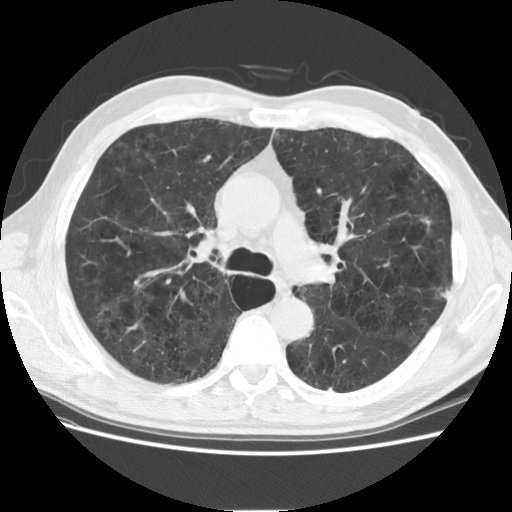
Axial slice from a low-dose chest CT screening exam; second screening round (one year after baseline); lung window (W 1500 / L -600 HU); 2.5 mm slice thickness; slice 70 of 180 in the series. Male participant, aged 58 years at enrolment. Current smoker at enrolment.
- Lesion marked by an expert reader, bounding box (x1, y1, x2, y2) in pixels: (415, 209, 446, 243).
- No non-calcified nodule or mass ≥4 mm was recorded by the screening reader at this exam.
- Official screen result: negative screen, minor abnormalities not suspicious for lung cancer.
- Later outcome: lung cancer diagnosed 389 days after this screen — adenocarcinoma, NOS, left upper lobe, stage IA (AJCC 6th edition), 9 mm at pathology.